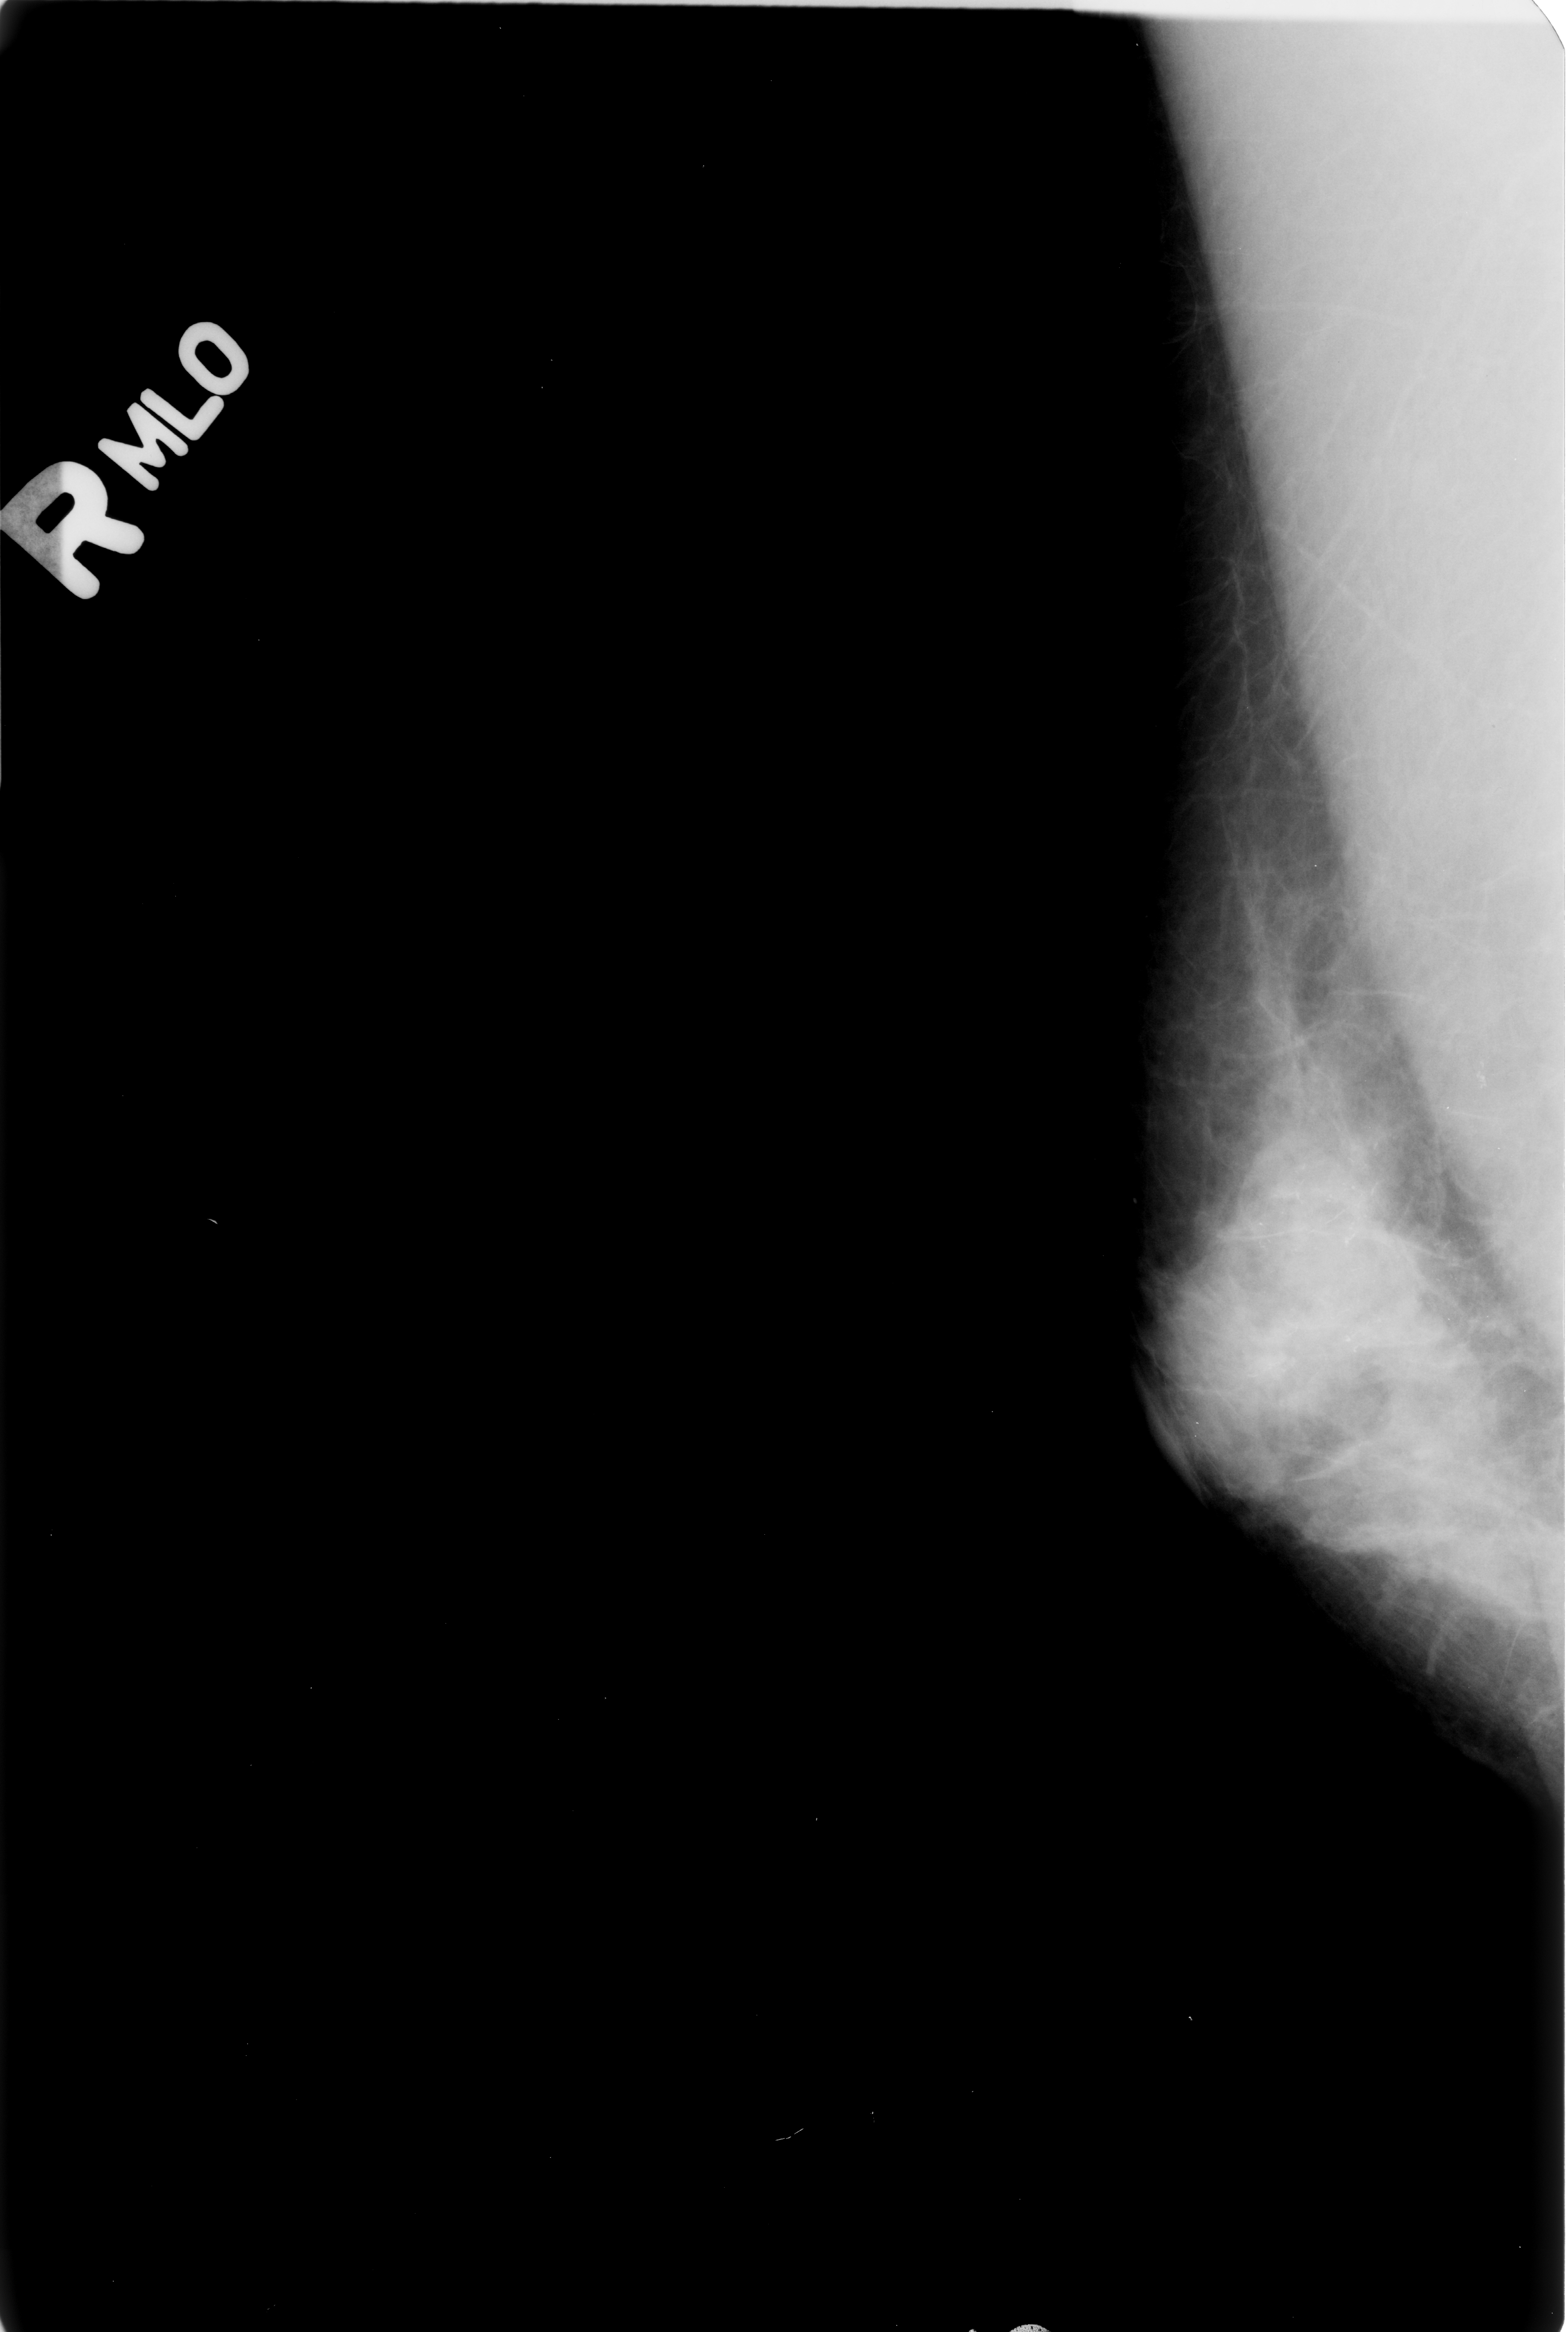
Mammogram (digitized film); right breast; MLO view; BI-RADS breast density category 3 (scale 1–4).
Radiologist-marked abnormalities on this image: calcifications, morphology fine linear branching, distribution segmental; BI-RADS assessment category 5; subtlety rating 3 on a 1 (subtle) to 5 (obvious) scale; pathology (as recorded): malignant.